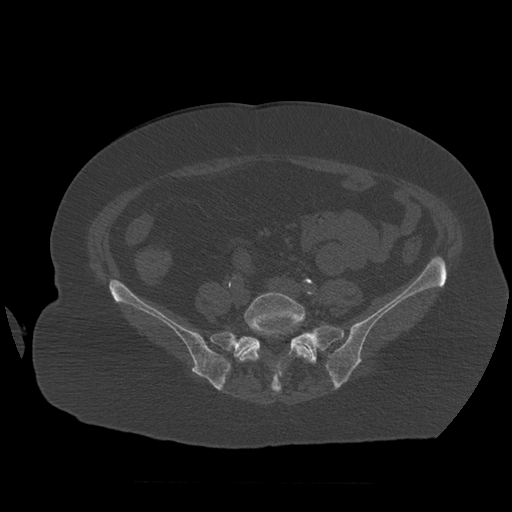
CT including the spine, one axial slice. Position 174 of 399 along the scan axis. Bone window (W 1800 / L 400 HU). 1.25 mm slice thickness. 512 × 512 image matrix, field of view 404 × 404 mm. Patient age 81 years. Case-level facts recorded for this patient, not image findings: primary cancer: renal; vertebrae with lytic lesions (as recorded): L1.
Annotated regions visible in this slice (semi-automatically segmented with operator editing):
- L5 vertebra: bounding box [x1, y1, x2, y2] px = [238, 292, 312, 362]